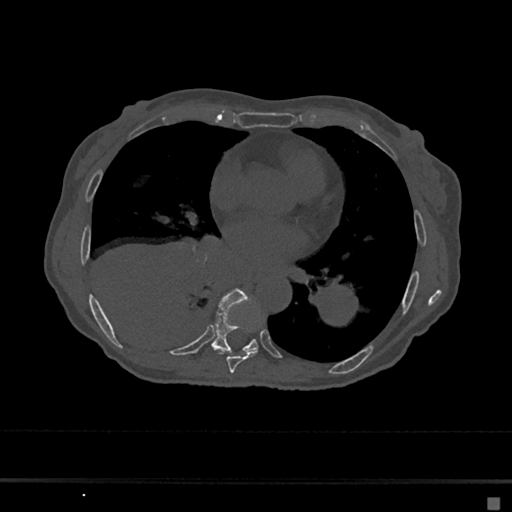
CT including the spine, one axial slice; position 348 of 797 along the scan axis; reconstruction kernel Br40s/3; bone window (W 1800 / L 400 HU); 0.5 mm slice thickness; 512 × 512 image matrix, field of view 360 × 360 mm. Patient: female, 68 years. From the clinical record (not read from this slice): primary cancer: renal.
Annotated regions visible in this slice (semi-automatically segmented with operator editing):
- T7 vertebra: bounding box [x1, y1, x2, y2] px = [218, 322, 262, 373]
- T8 vertebra: [211, 288, 259, 354]